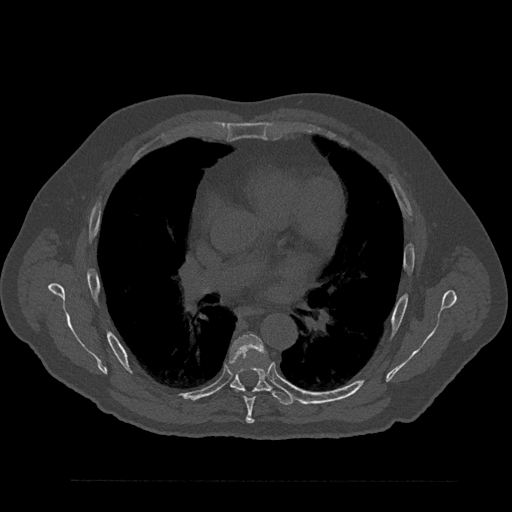
CT including the spine, one axial slice. Slice 531 of 797 in the series (ordered by position). 120 kVp. Bone window (W 1800 / L 400 HU). 0.5 mm slice thickness. 512 × 512 image matrix. Male patient, age 61 years. Case-level facts recorded for this patient, not image findings: primary cancer: prostate.
Annotated regions visible in this slice (semi-automatically segmented with operator editing):
- T6 vertebra: bounding box <230,335,266,424> (left, top, right, bottom; pixels)
- T7 vertebra: <230,366,293,405>